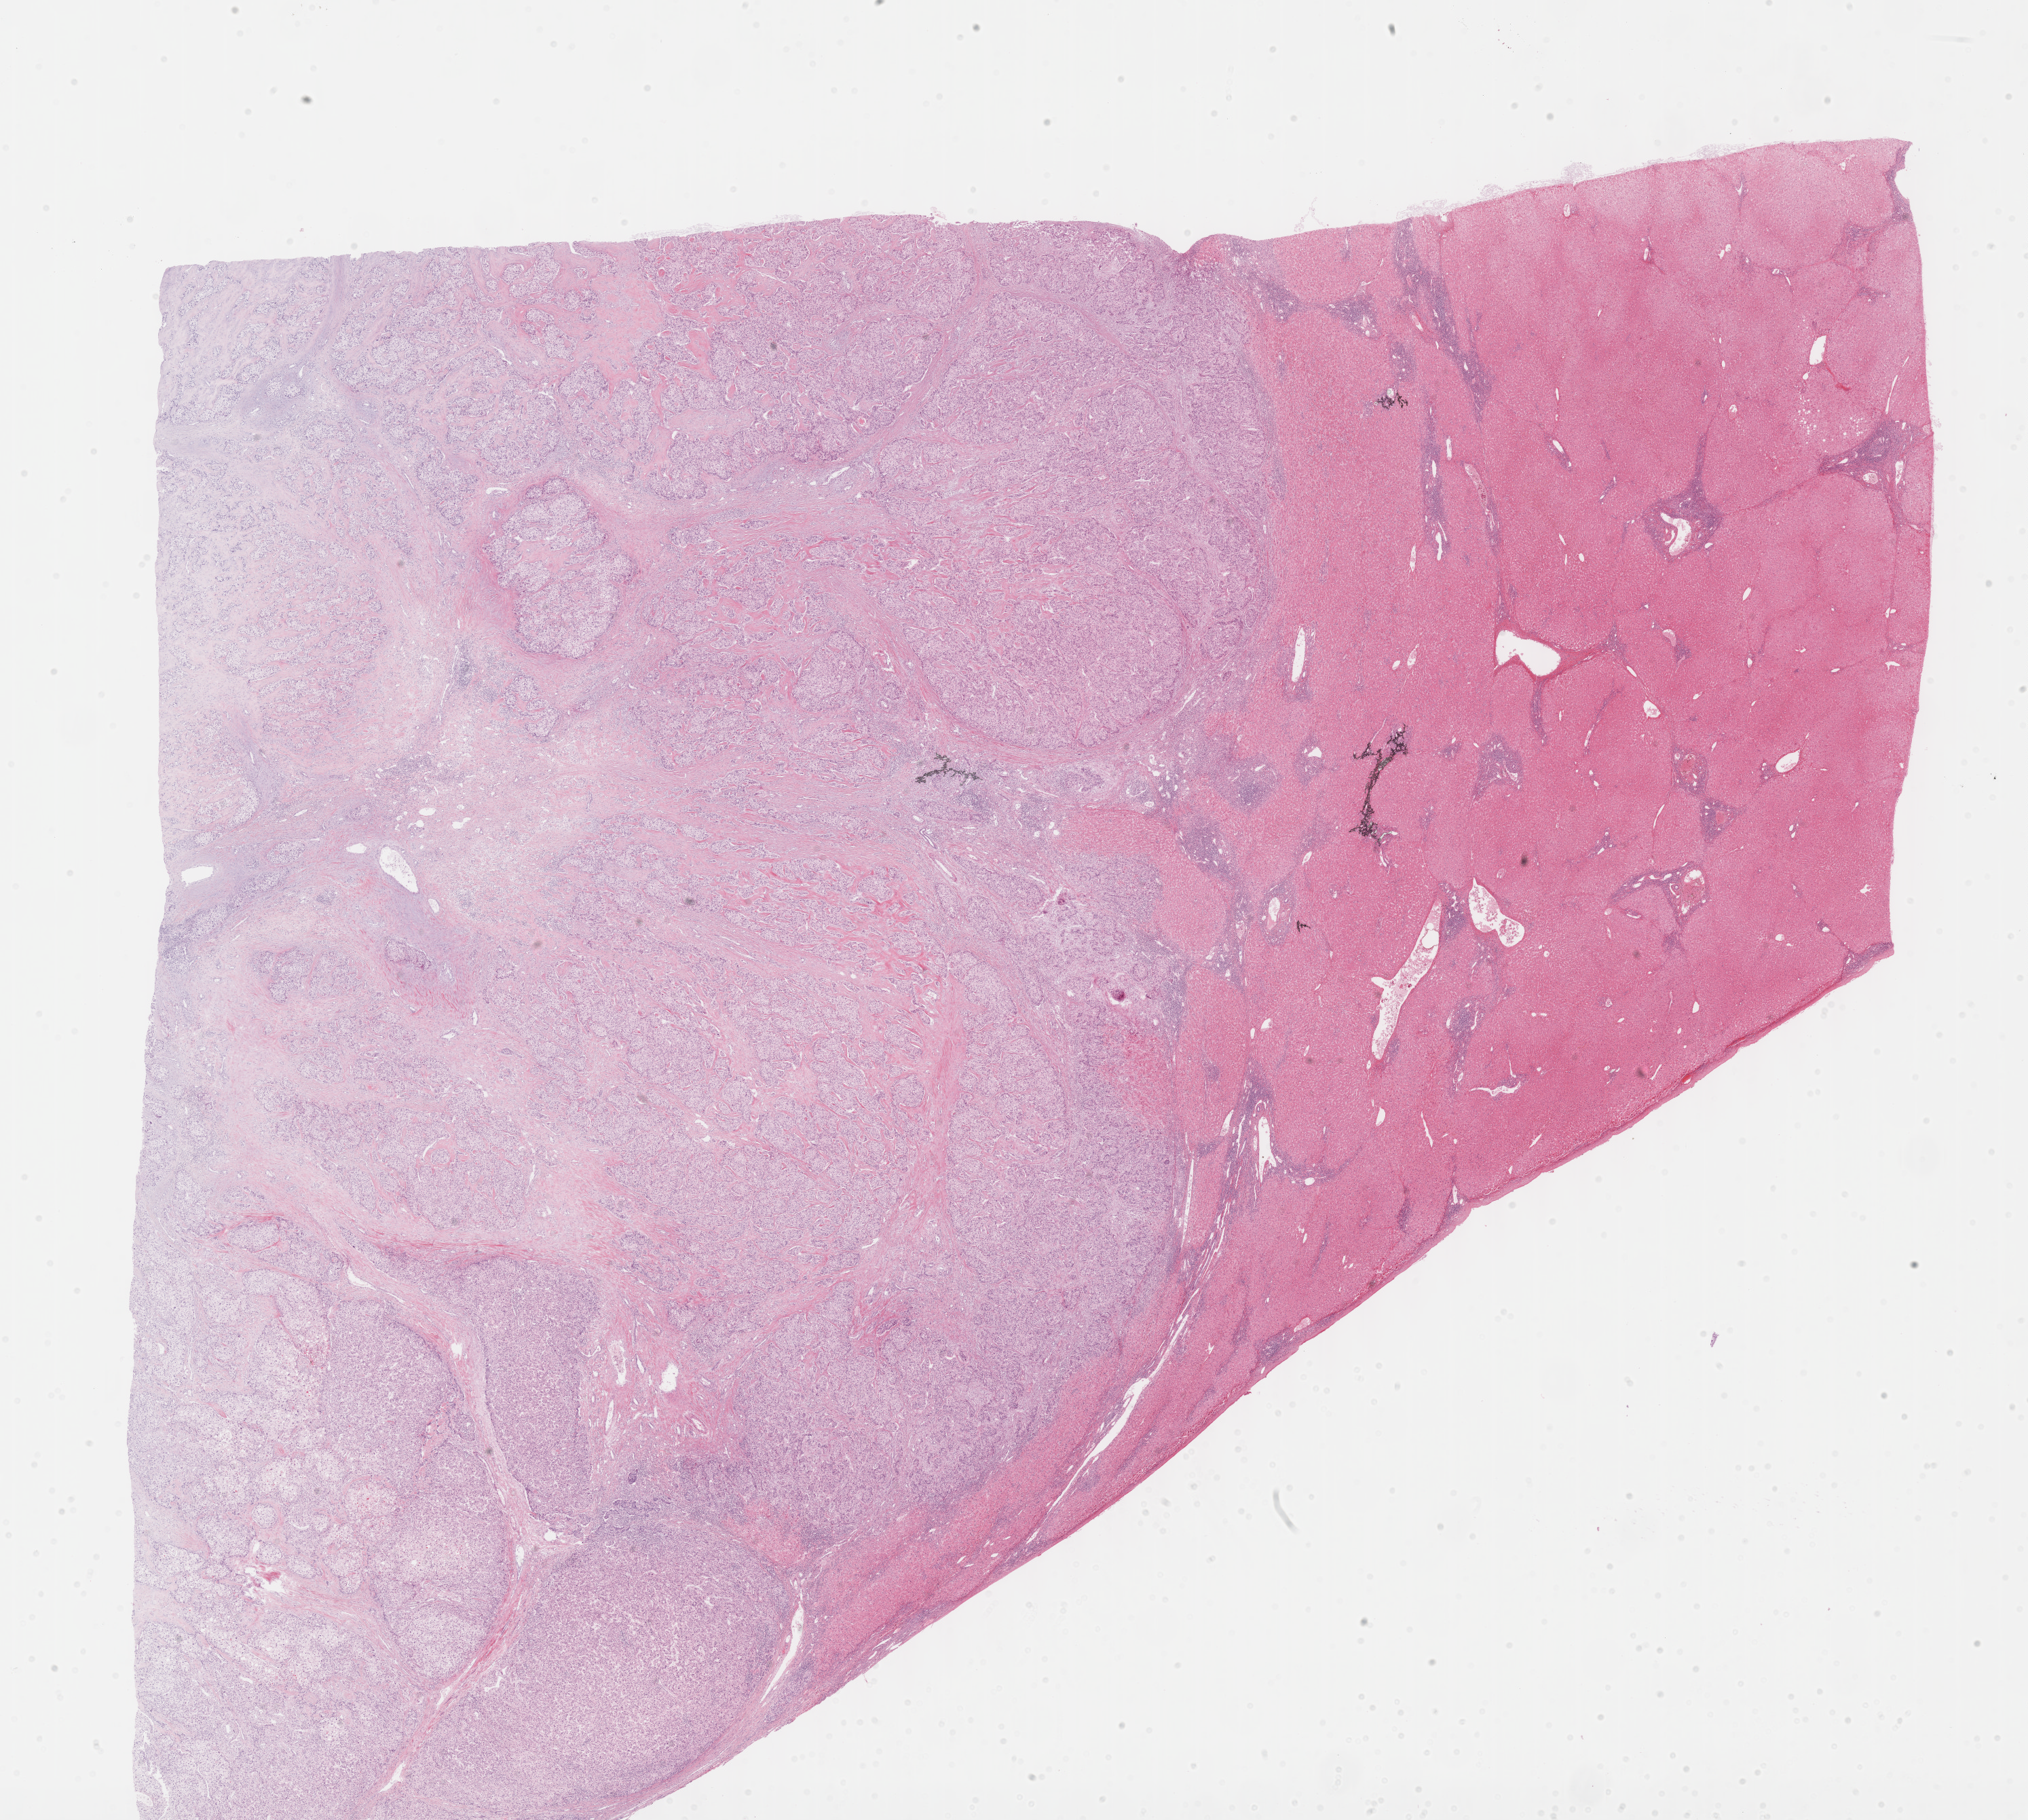
H&E-stained whole-slide image — whole scanned area (about 24.1 x 21.7 mm, acquisition: 40x scan) shown as a low-resolution overview. Formalin-fixed paraffin-embedded (FFPE) diagnostic section. Primary tumour sample from the liver. Male, age 42 years at initial diagnosis. Histologic grade: G3 (poorly differentiated).
Pathologic diagnosis: Hepatocellular carcinoma, clear cell type. AJCC pathologic stage: II.